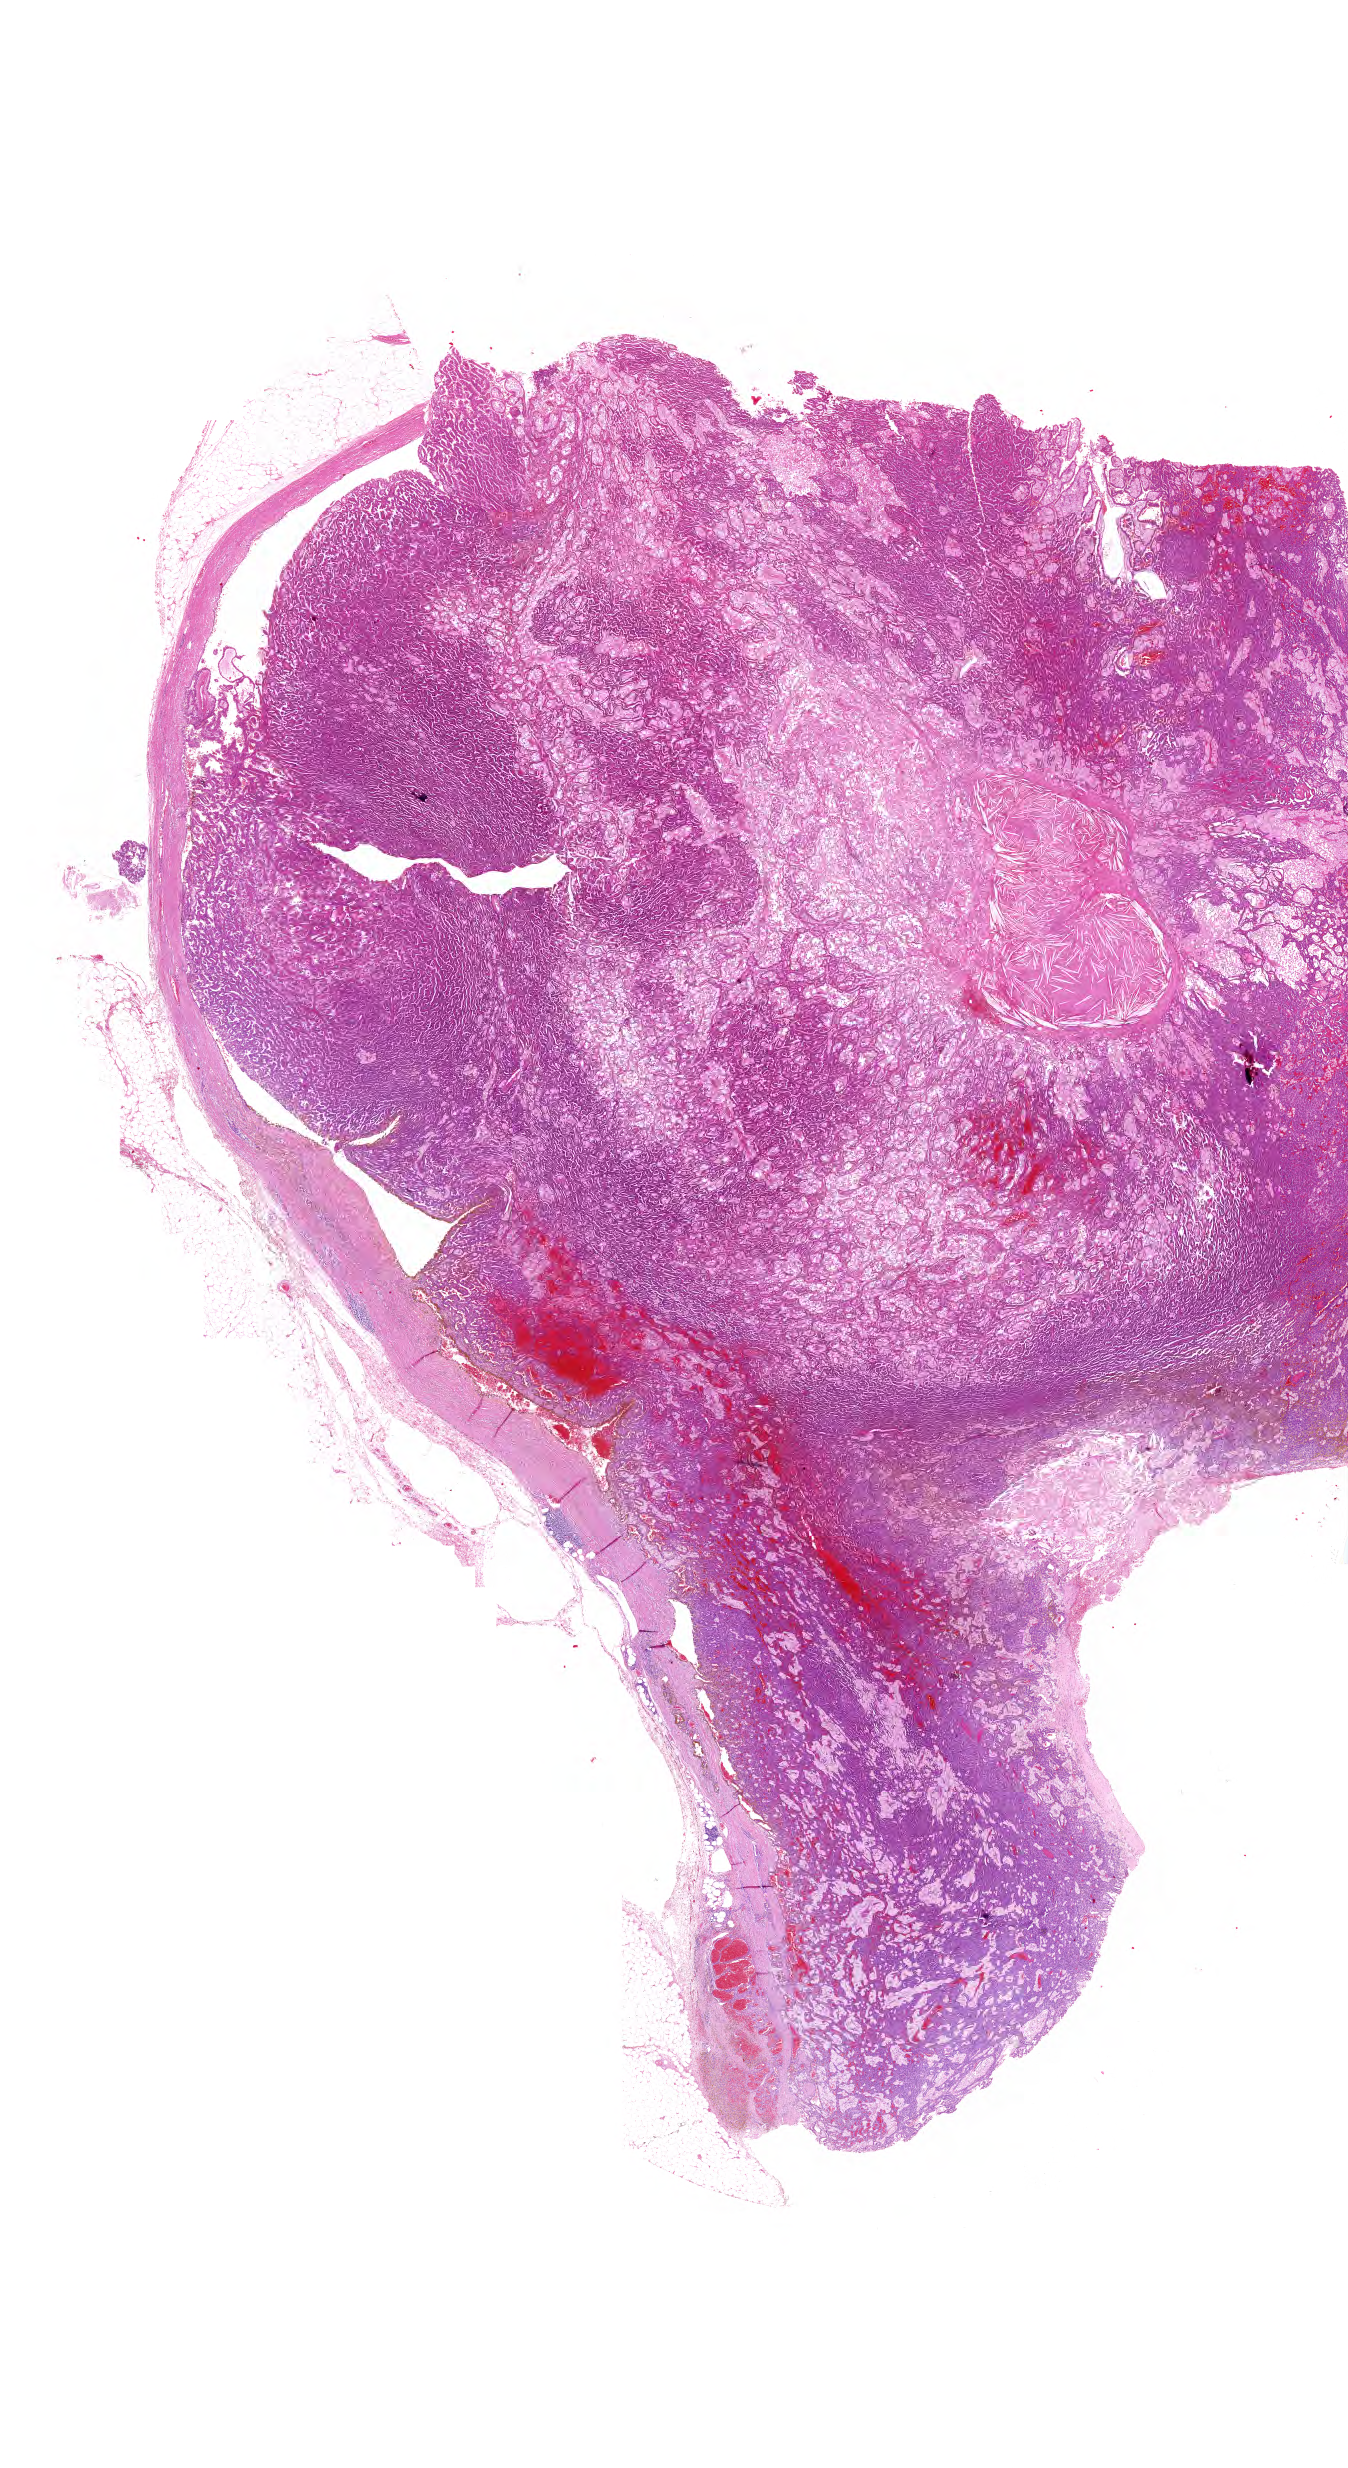
H&E-stained whole-slide image, a low-resolution overview of the entire scanned area, about 16.8 x 30.7 mm; formalin-fixed paraffin-embedded (FFPE) diagnostic section; primary tumour sample from the kidney. Female patient; age at initial diagnosis 51 years.
Histologic diagnosis: Papillary adenocarcinoma, NOS.